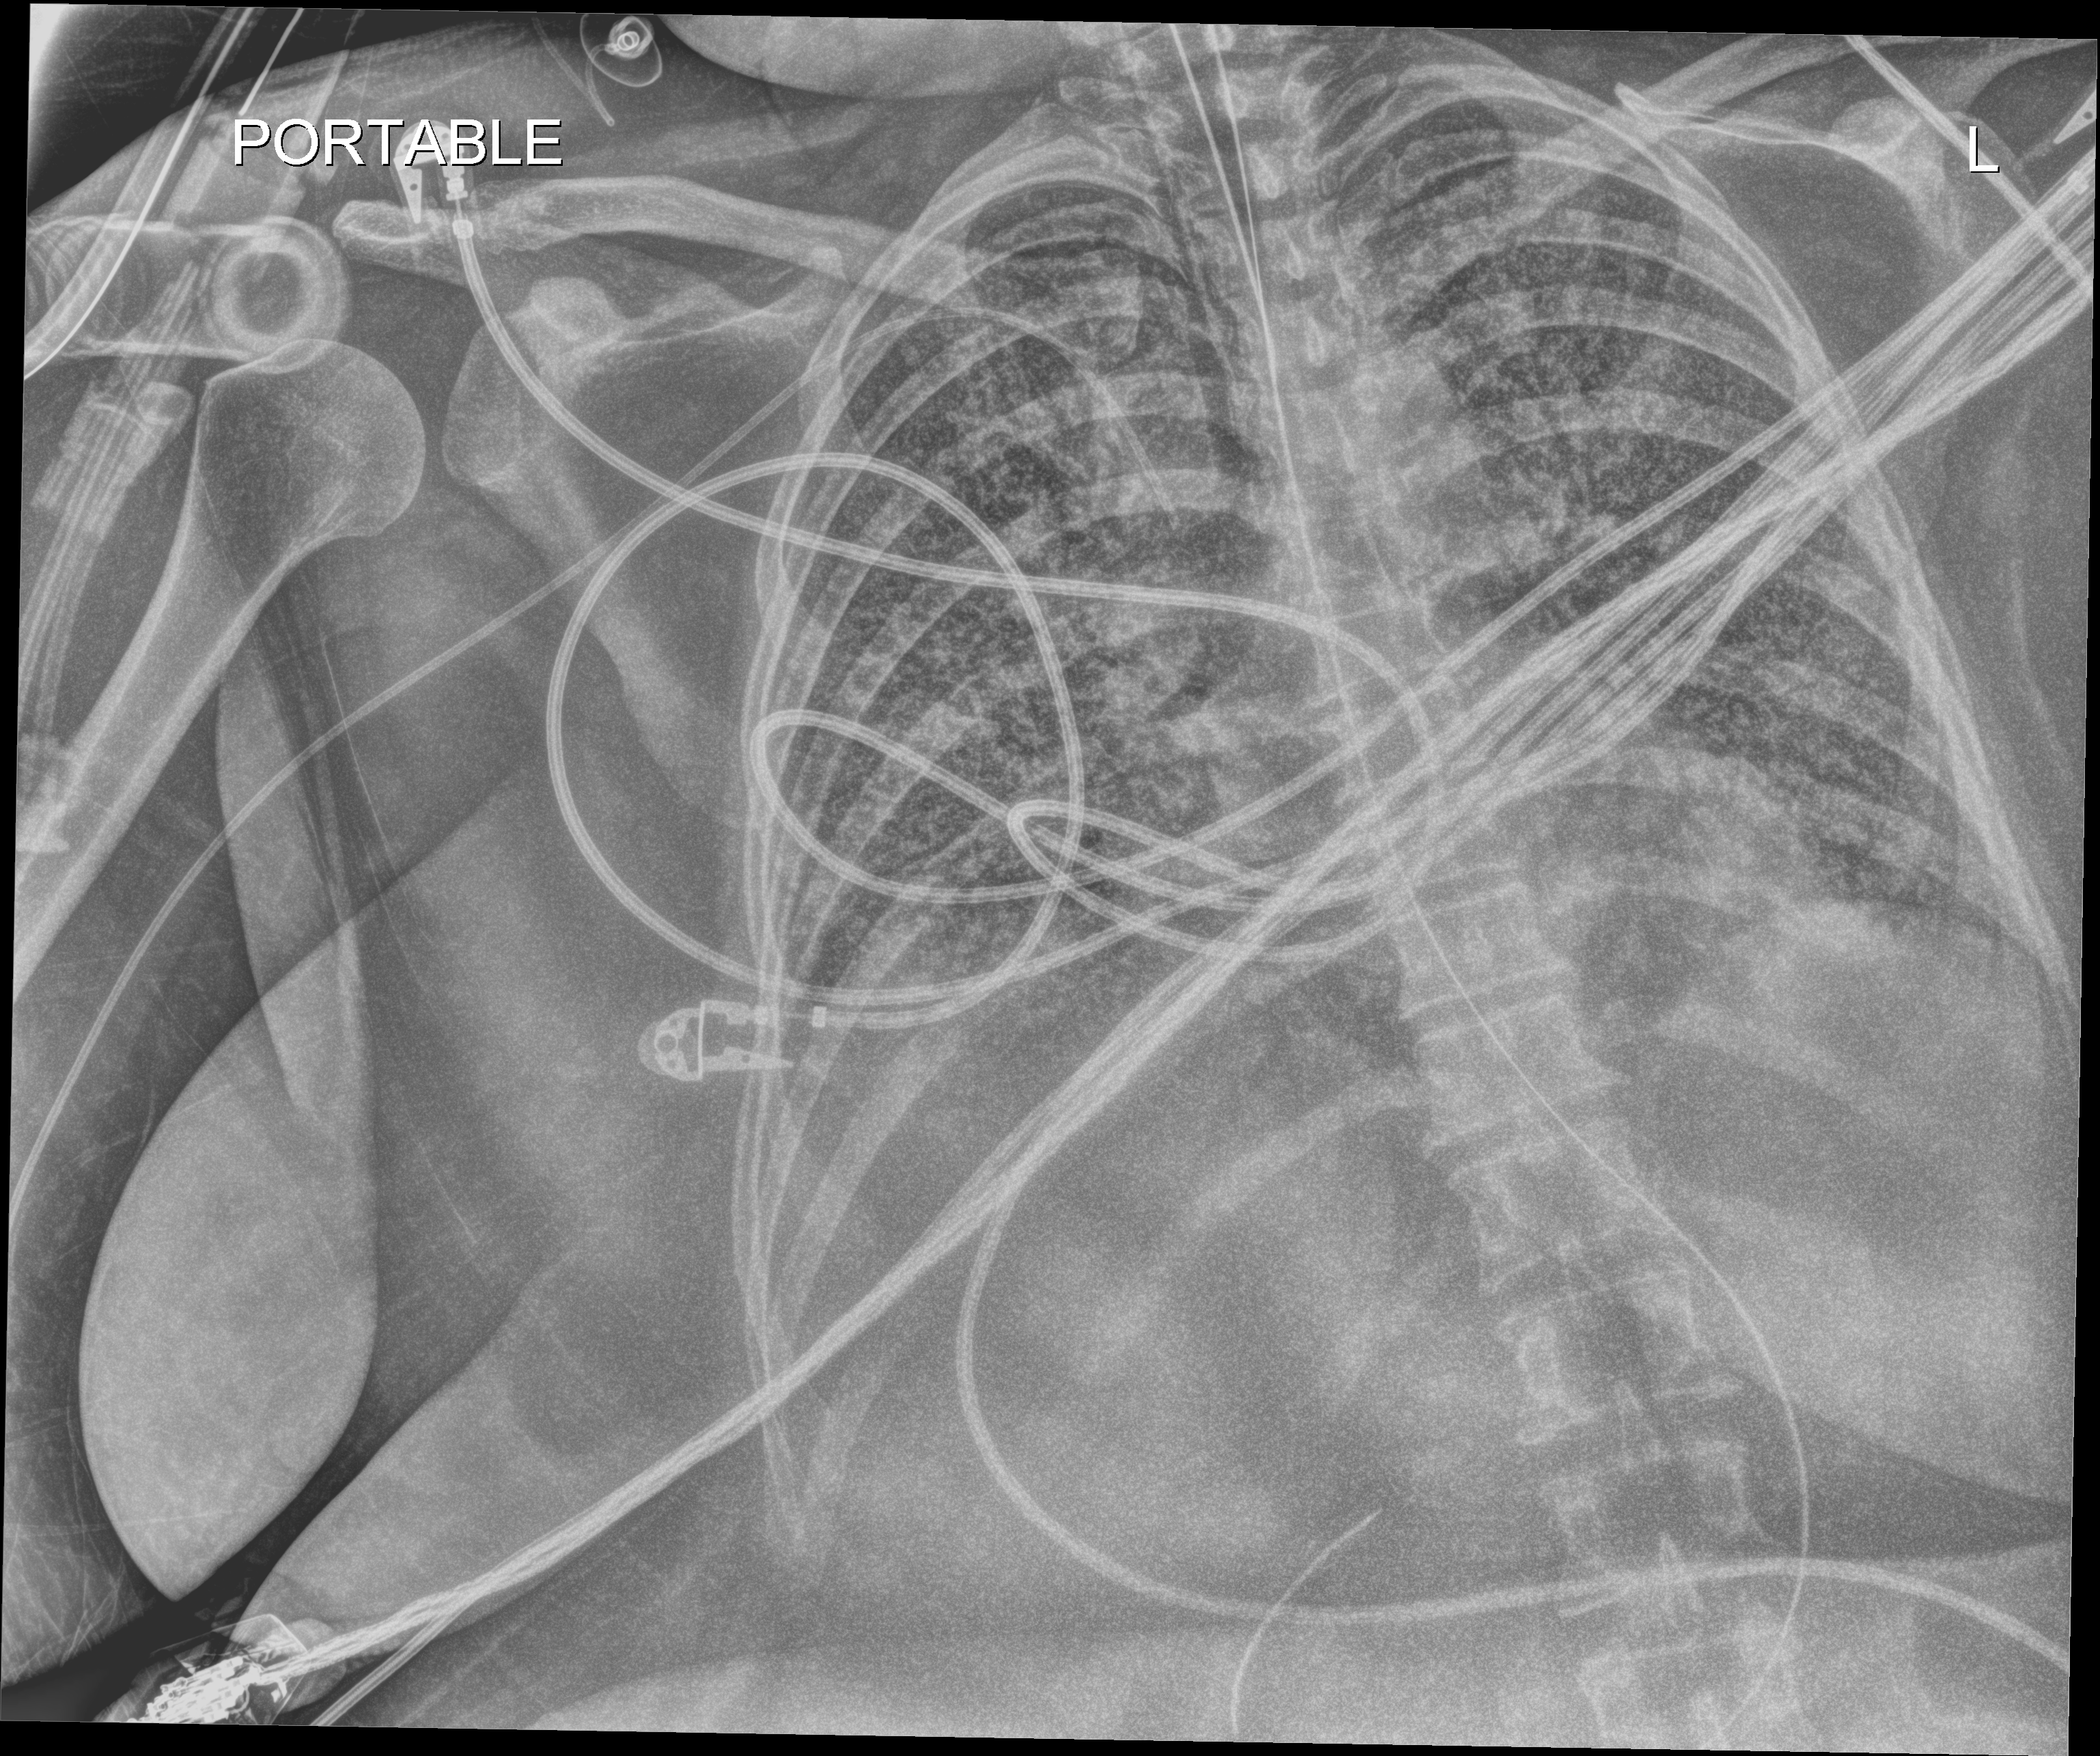
Bedside chest radiograph (digital radiography), anteroposterior (AP) projection. Female patient hospitalised with COVID-19, age 18–59 years.
Admission-level facts for this patient (not findings on this image; timing relative to this image not recorded):
- other chronic lung disease (admission record): no
- length of hospital stay: 95 days
- admitted to intensive care during this hospital stay: yes